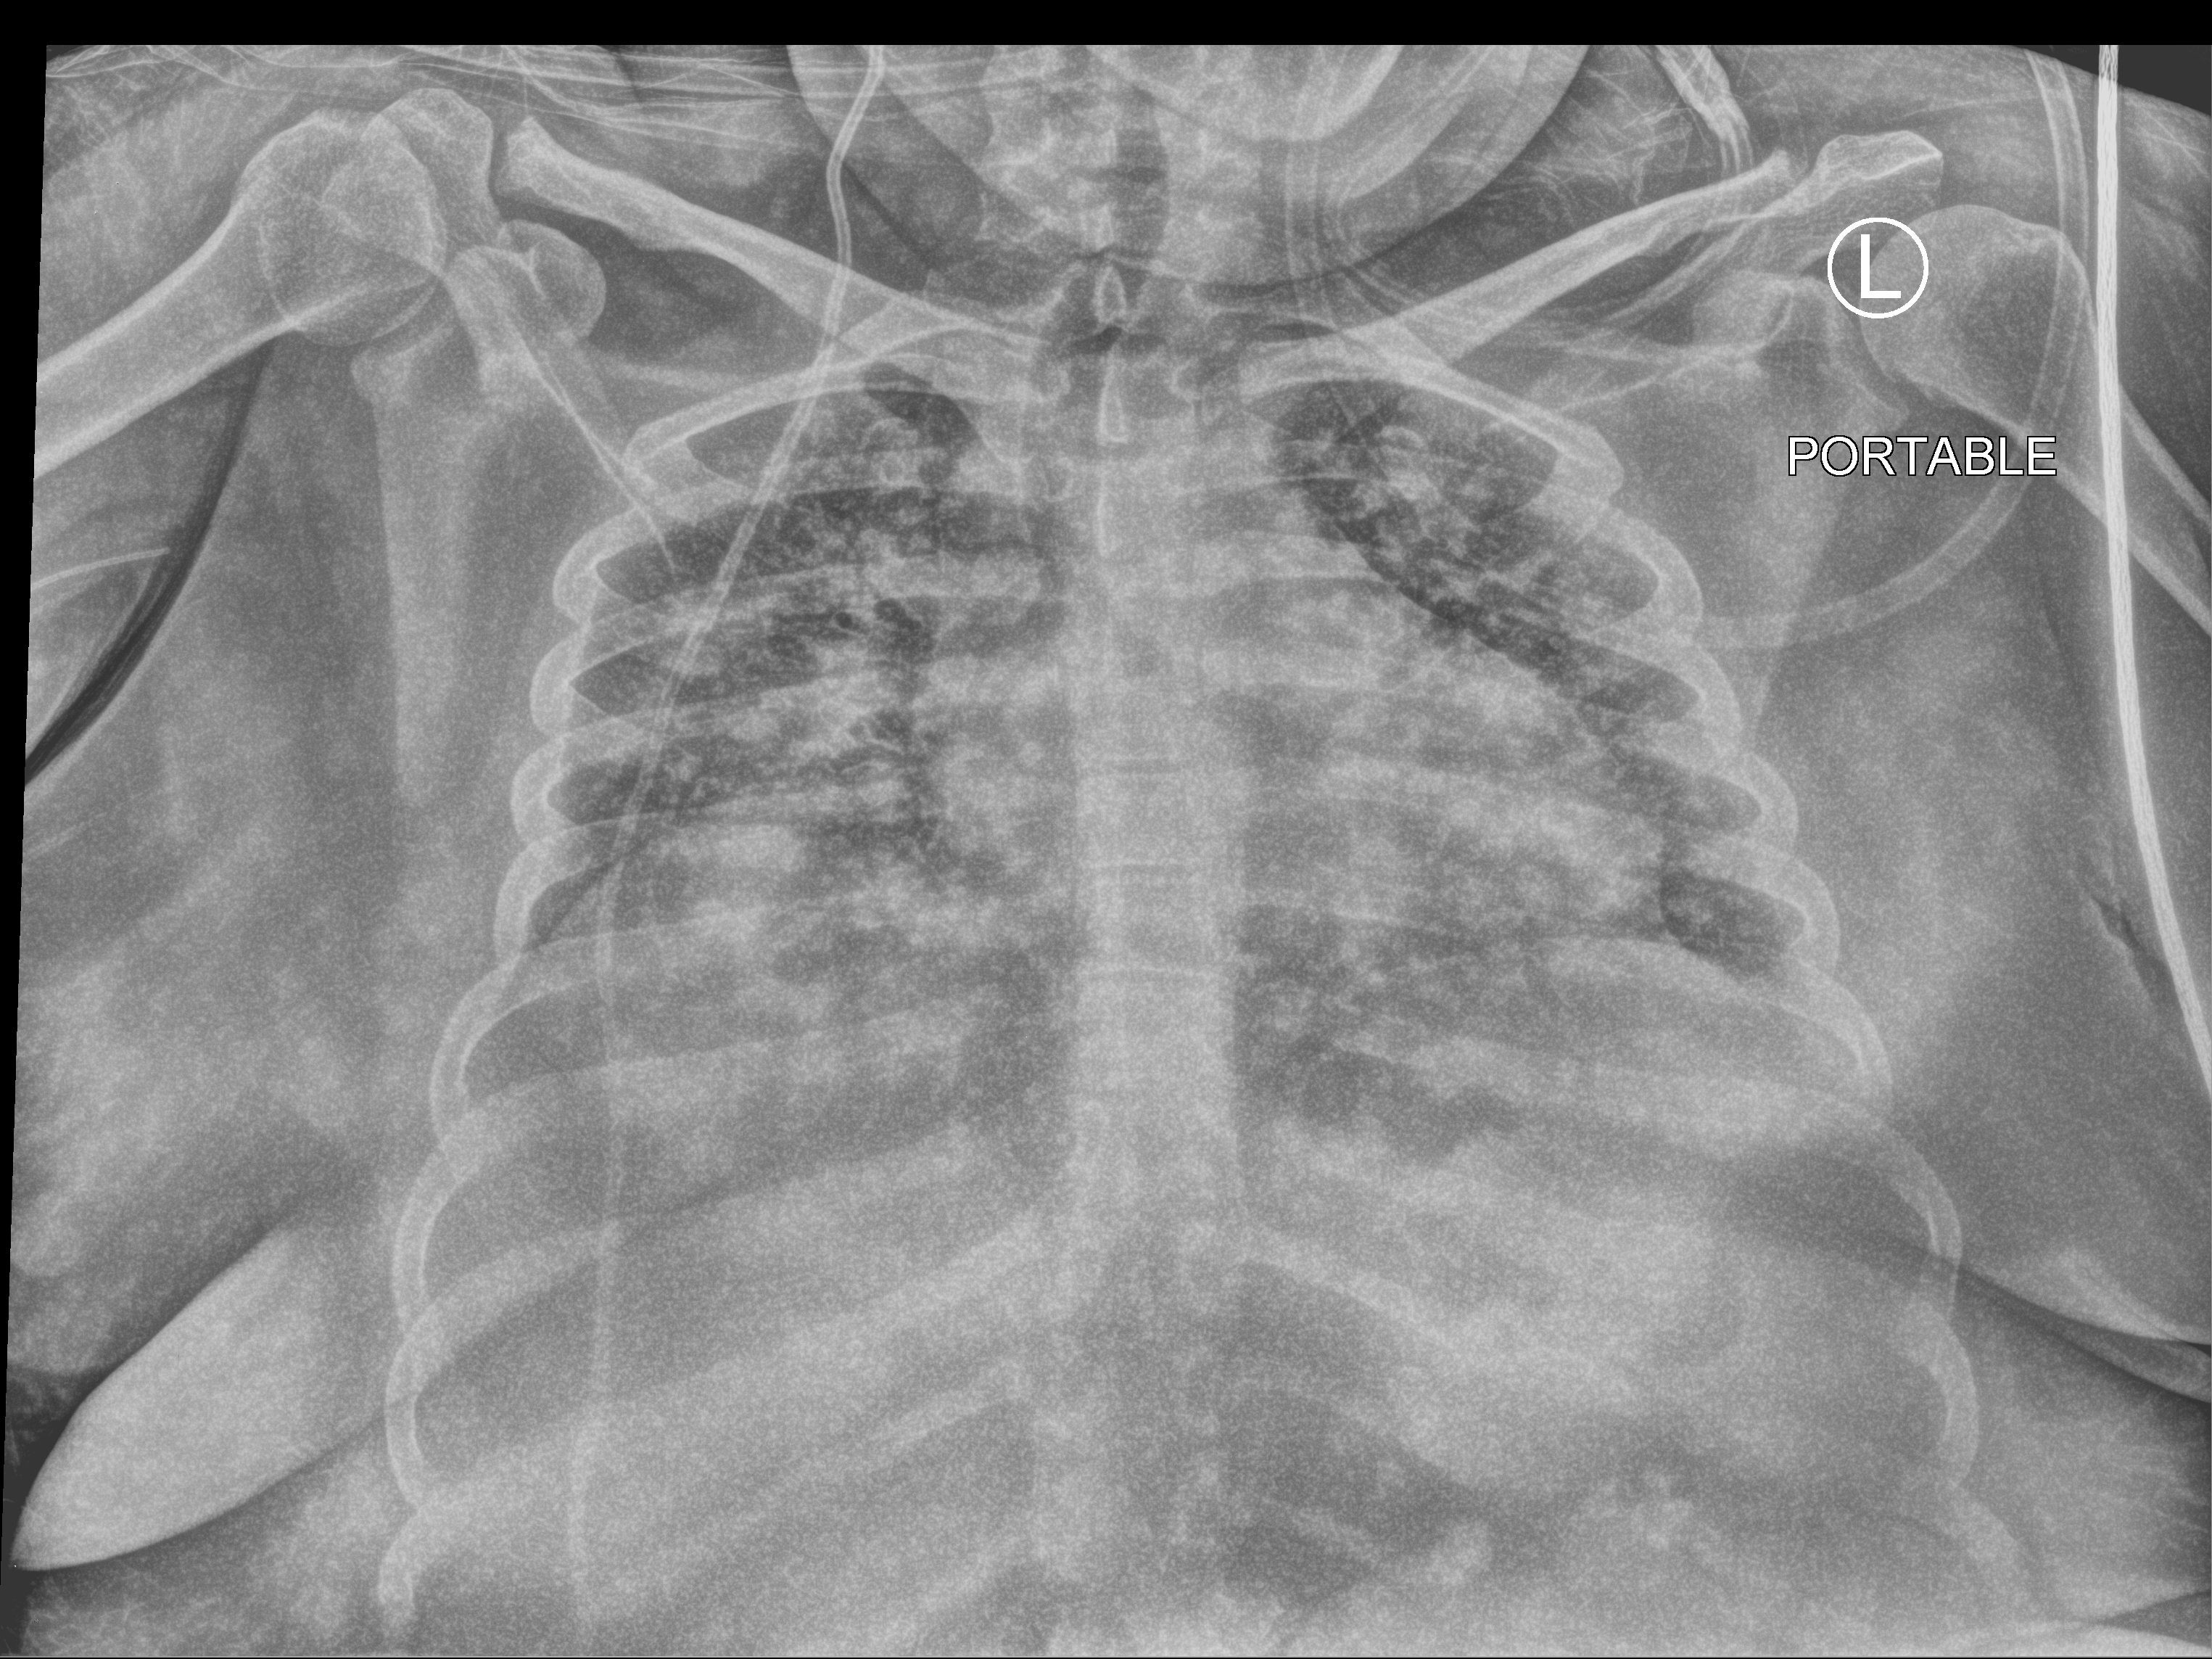
Chest X-ray (portable), anteroposterior (AP) projection. Female patient hospitalised with COVID-19, age 18–59 years.
Admission-level facts for this patient (not findings on this image; timing relative to this image not recorded): mechanically ventilated during this hospital stay: no.